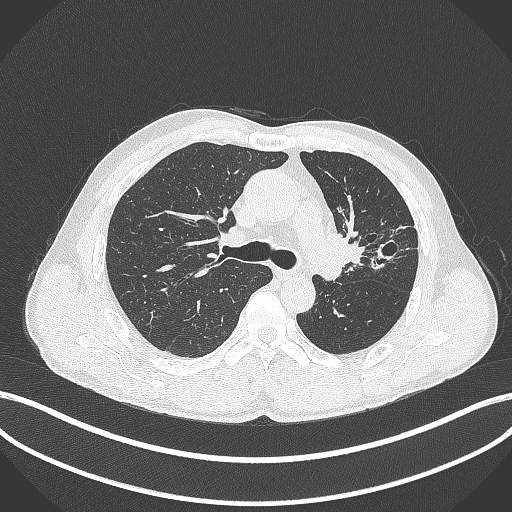
Chest CT, one axial slice; position 271 of 429 along the scan axis; 120 kVp; lung window (W 1500 / L -600 HU); 512 × 512 image matrix, field of view 400 × 400 mm. Patient: male, 57 years. From the clinical record (not read from this slice): clinical TNM (as recorded): T2b N0 M0.
Annotated regions visible in this slice (rectangle marked by the reading radiologist):
- lung tumour (recorded histology: squamous cell carcinoma): bounding box [x1, y1, x2, y2] px = [325, 224, 368, 268]